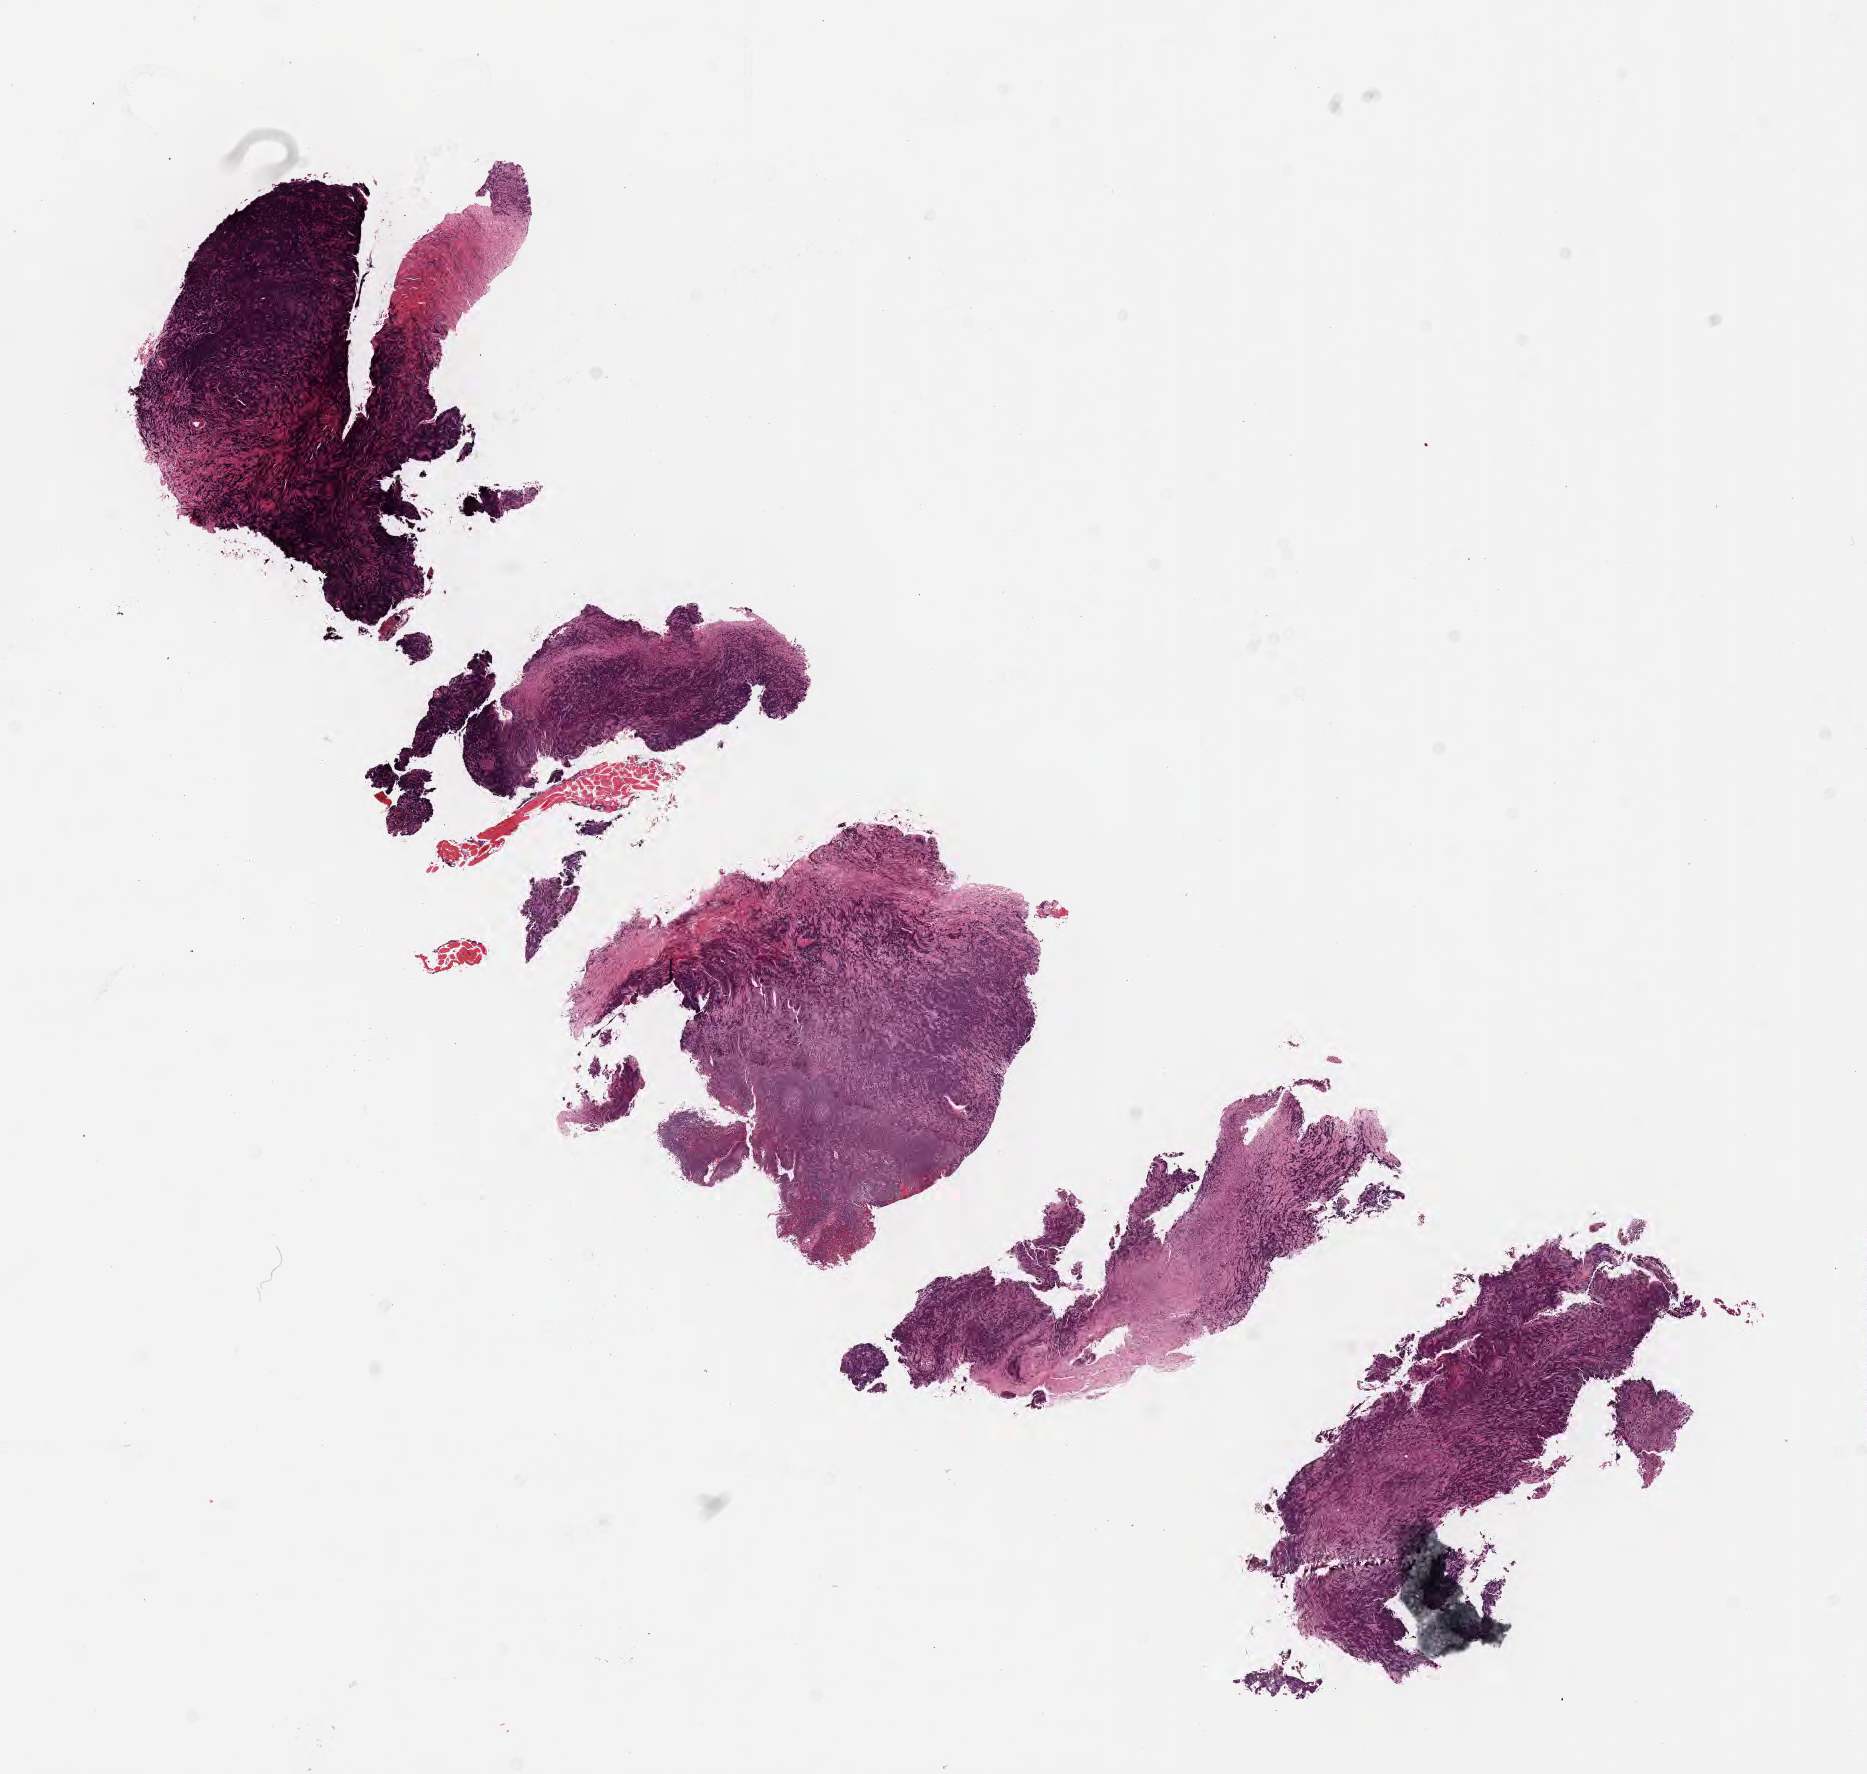
Digitized H&E-stained section, whole scanned area (about 15.1 x 14.3 mm) shown as a low-resolution overview; FFPE section; primary tumor. Patient: female, aged 38. Pathologist review of this section (percent, as recorded): tumor cells 40%, tumor nuclei 60%.
Diagnosis: Burkitt lymphoma, NOS.